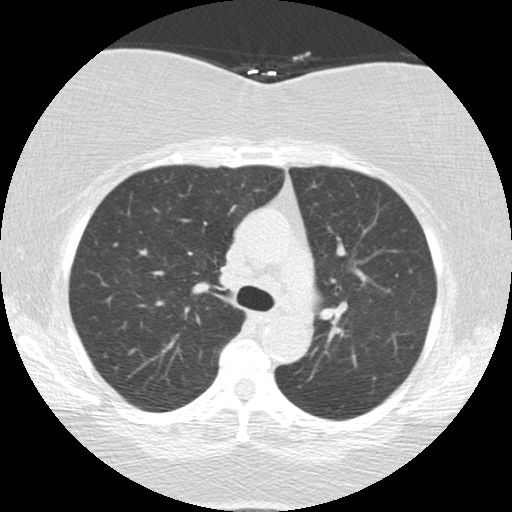
Low-dose screening chest CT, one axial slice; position 91 of 136 along the scan axis; 120 kVp; lung window (W 1500 / L -600 HU); 512 × 512 image matrix, field of view 309 × 309 mm.
Outlined on this slice (expert manual segmentation):
- lesion 1 (tumor, lower lobe of left lung): bounding box [x1, y1, x2, y2] px = [220, 265, 245, 285]